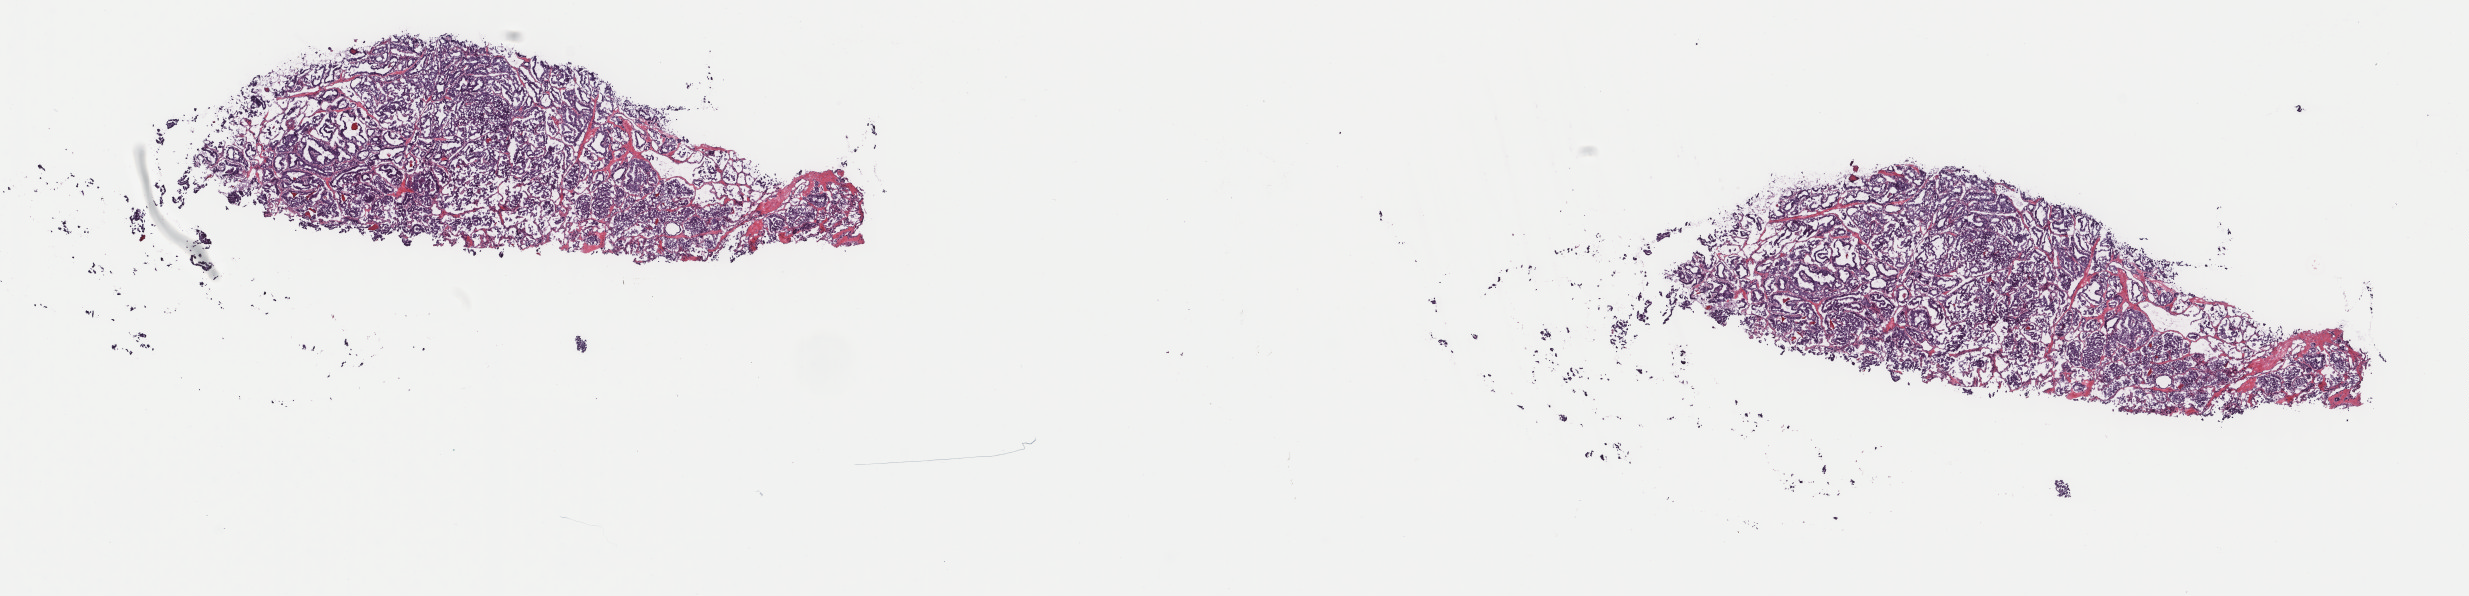
Digitized H&E tissue section (whole slide), low-resolution overview of the scanned area, about 19.6 x 4.7 mm (acquisition: 40x scan), frozen section from the top of the tissue portion, primary tumour sample from the thyroid. Male, age 28 years at initial diagnosis.
Pathologic diagnosis: Papillary adenocarcinoma, NOS (thyroid gland).